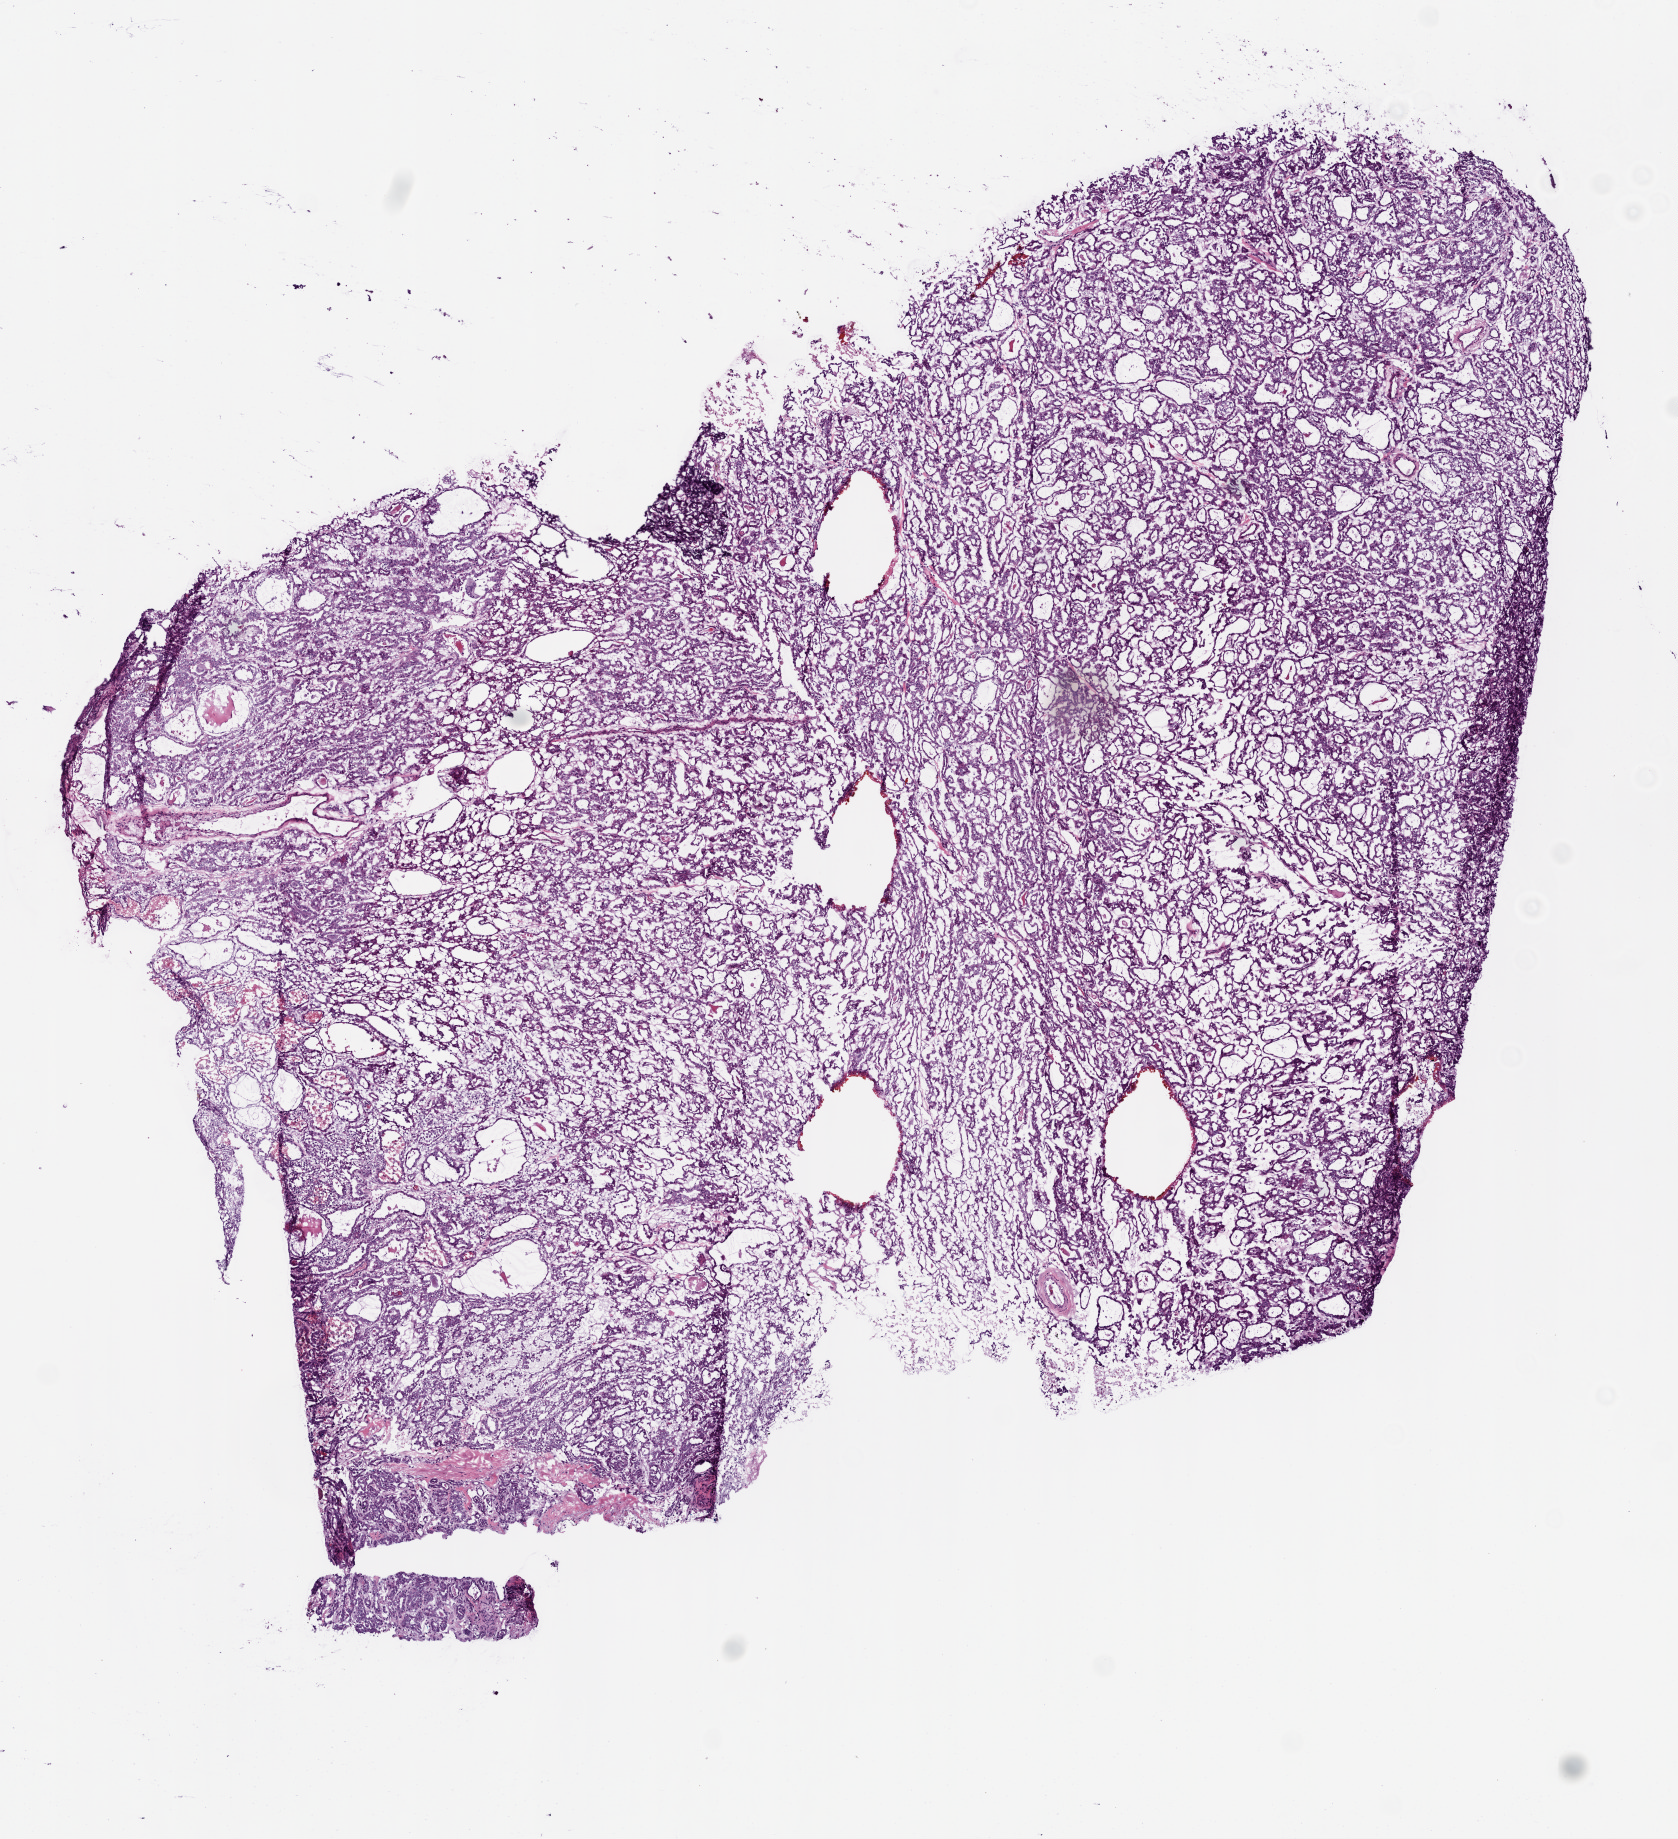
Digitized H&E tissue section (whole slide) — low-resolution overview of the scanned area, about 6.8 x 7.4 mm; frozen section from the top of the tissue portion; primary tumour sample from the thyroid. Female patient; age at initial diagnosis 48 years. Composition of this section per pathologist review: tumour cells 80%, tumour nuclei 80%, normal cells 10%, stromal cells 10%, necrosis 0%. Infiltration values recorded for this section: lymphocyte infiltration 0%, monocyte infiltration 0%, neutrophil infiltration 0%.
• AJCC pathologic stage: III (7th edition)
• diagnosis: Papillary adenocarcinoma, NOS (thyroid gland)
• laterality: right